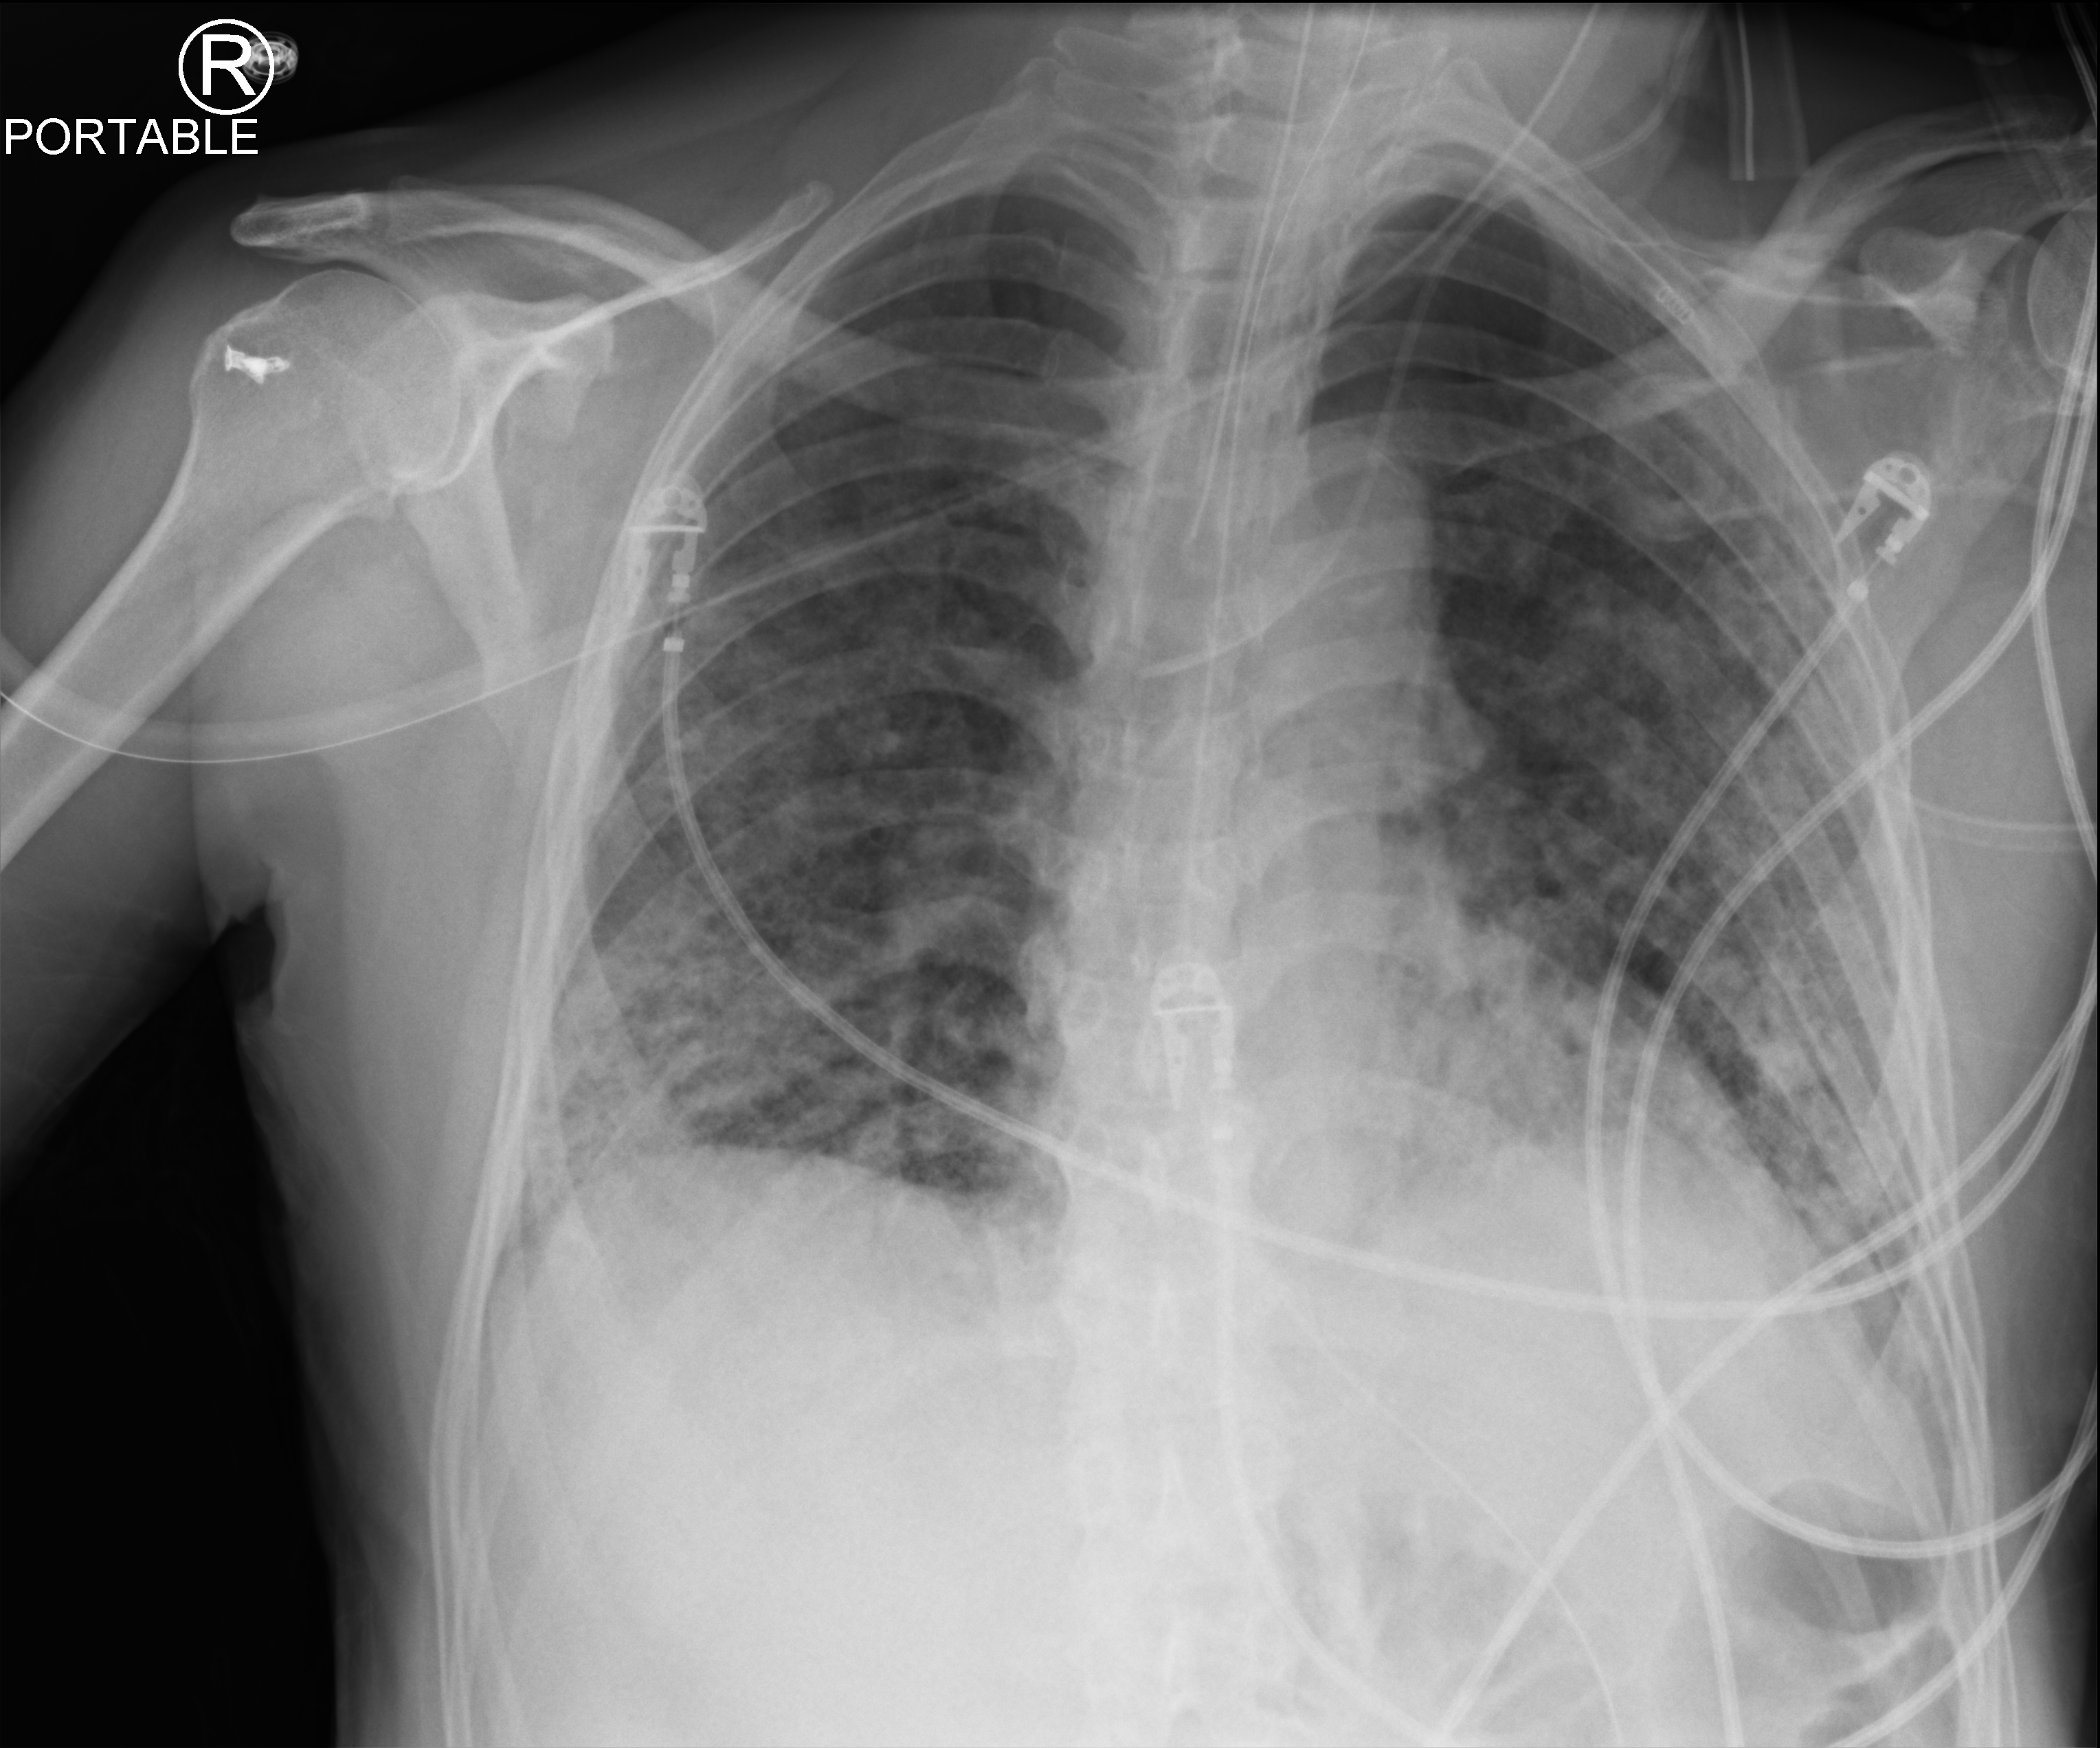
Chest X-ray (portable); anteroposterior (AP) projection. Male patient hospitalised with COVID-19, age 60–74 years.
Hospital-stay facts (about this admission, not read from this image; timing relative to this image not recorded):
- admitted to intensive care during this hospital stay: yes
- length of hospital stay: 65 days